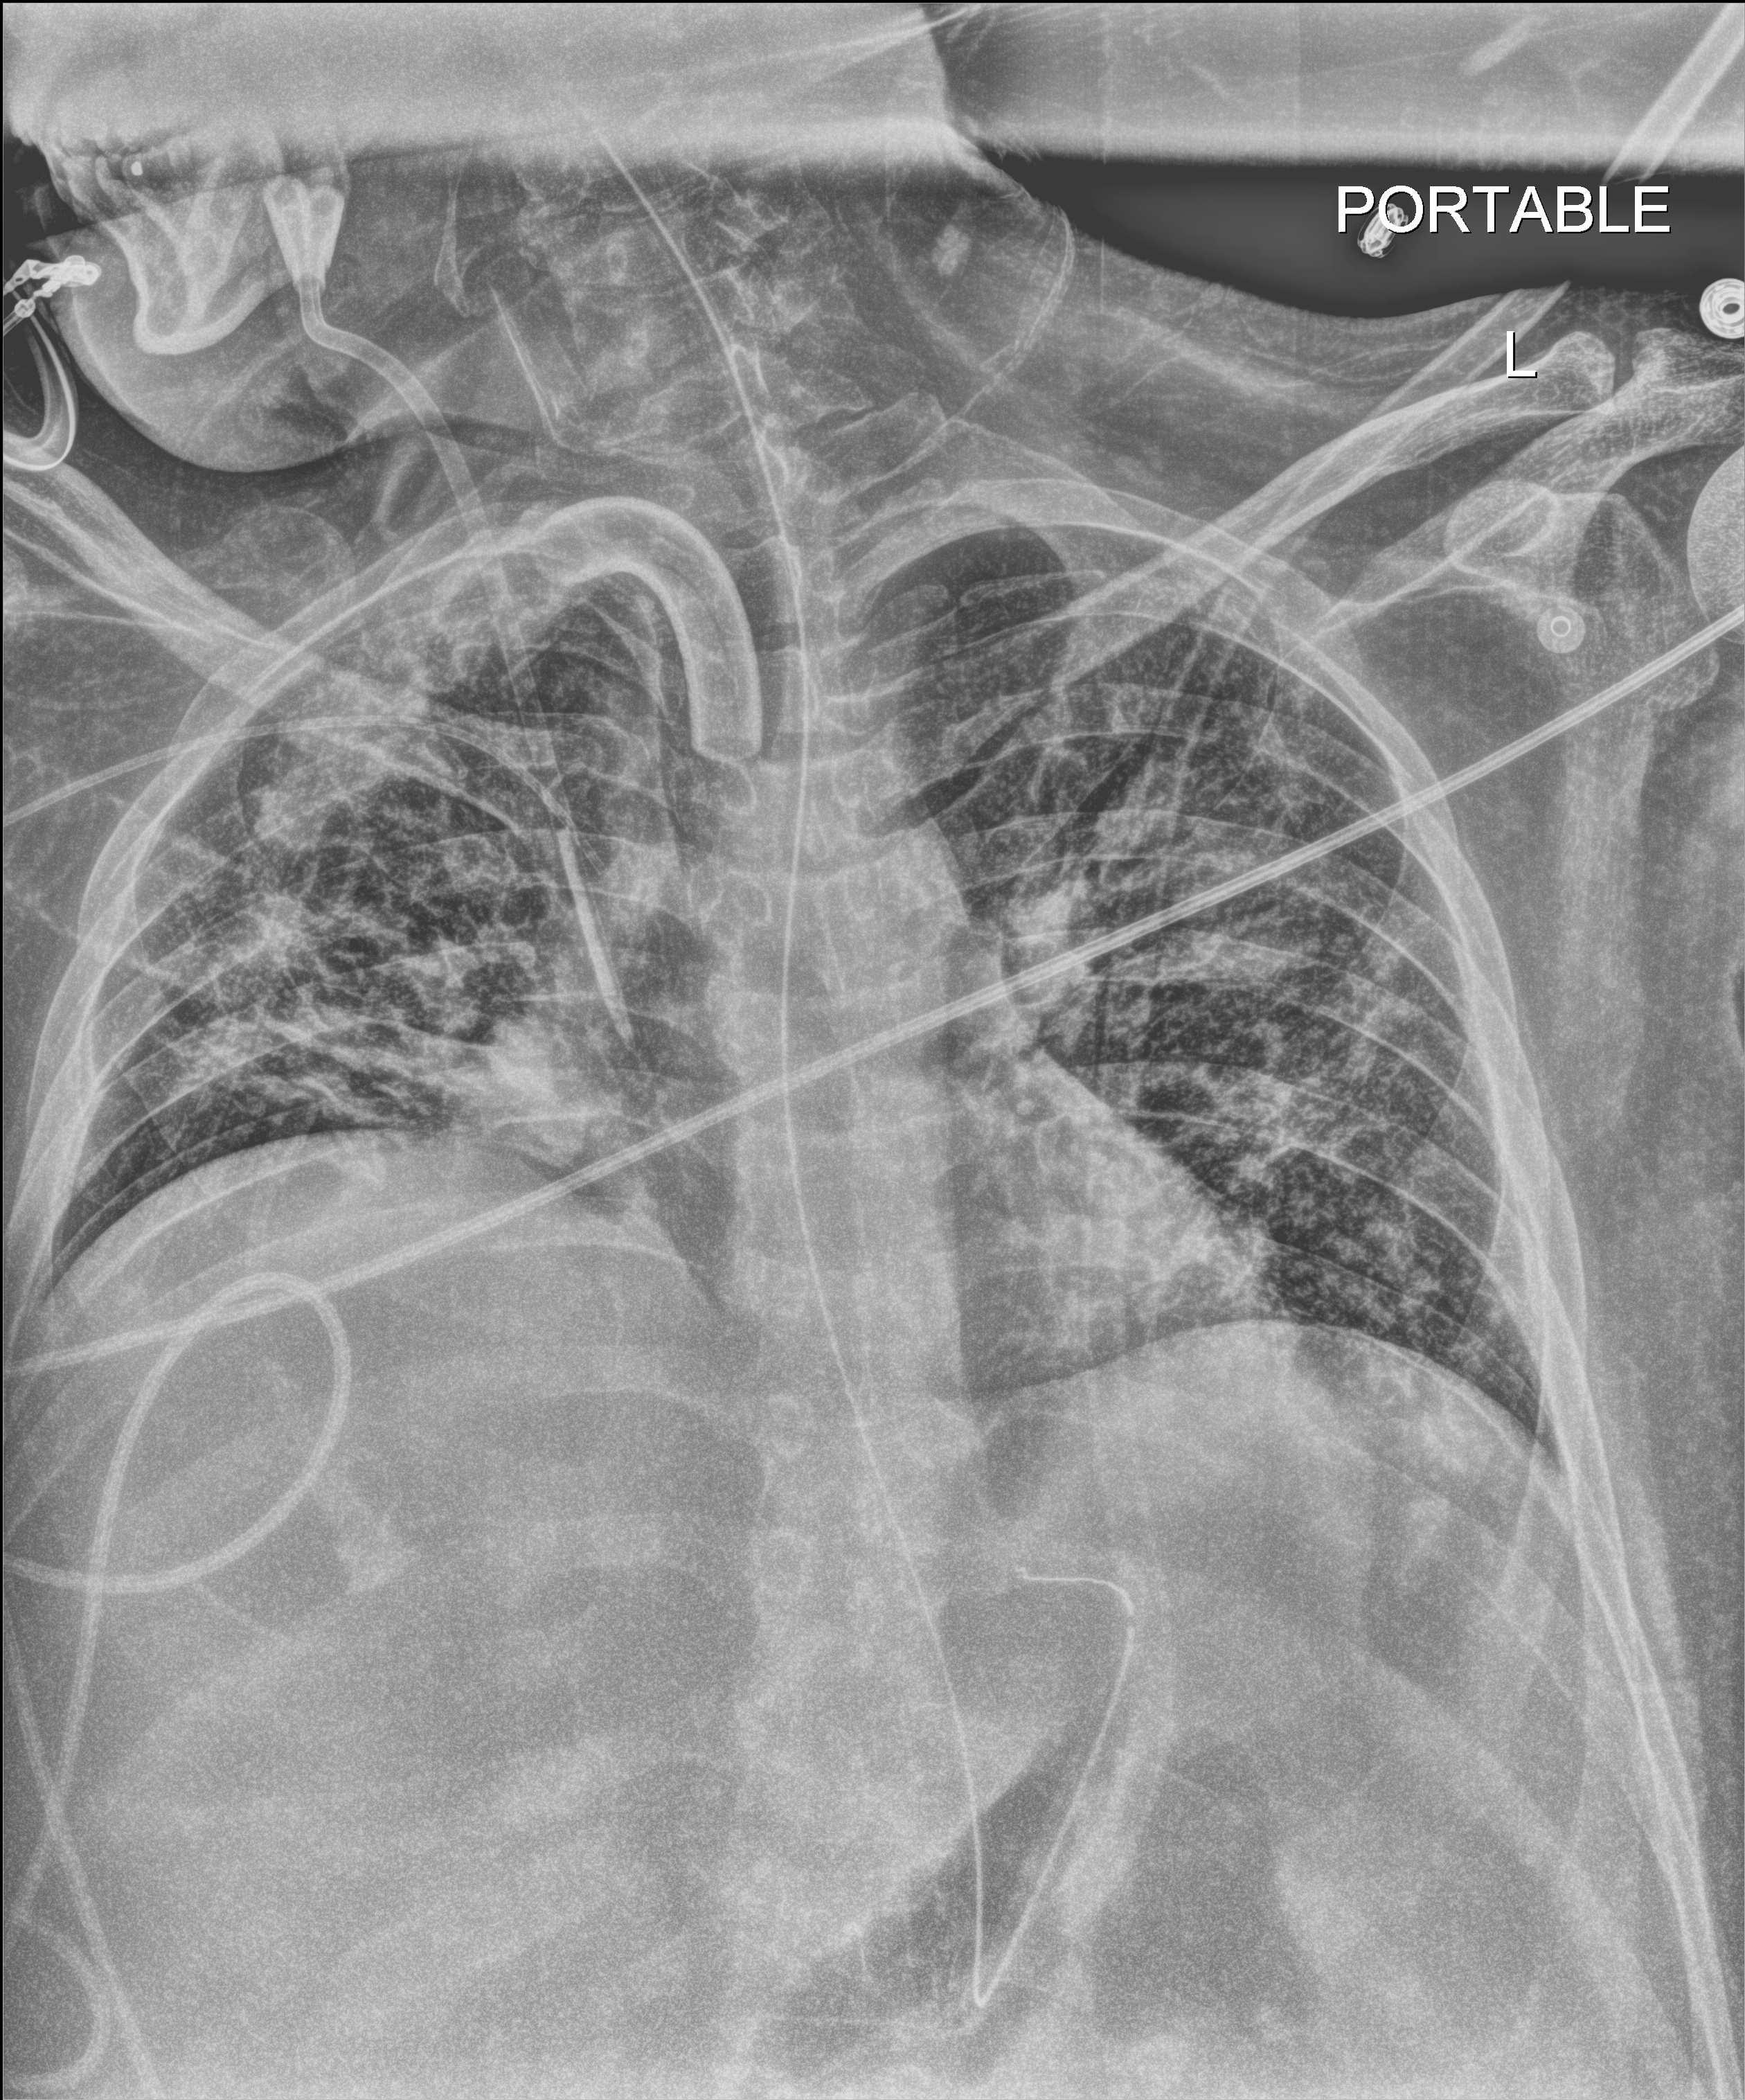
Portable chest radiograph, anteroposterior (AP) projection. Patient hospitalised with COVID-19, aged 18–59 years.
Hospital-stay facts (about this admission, not read from this image; timing relative to this image not recorded): mechanically ventilated during this hospital stay: yes.